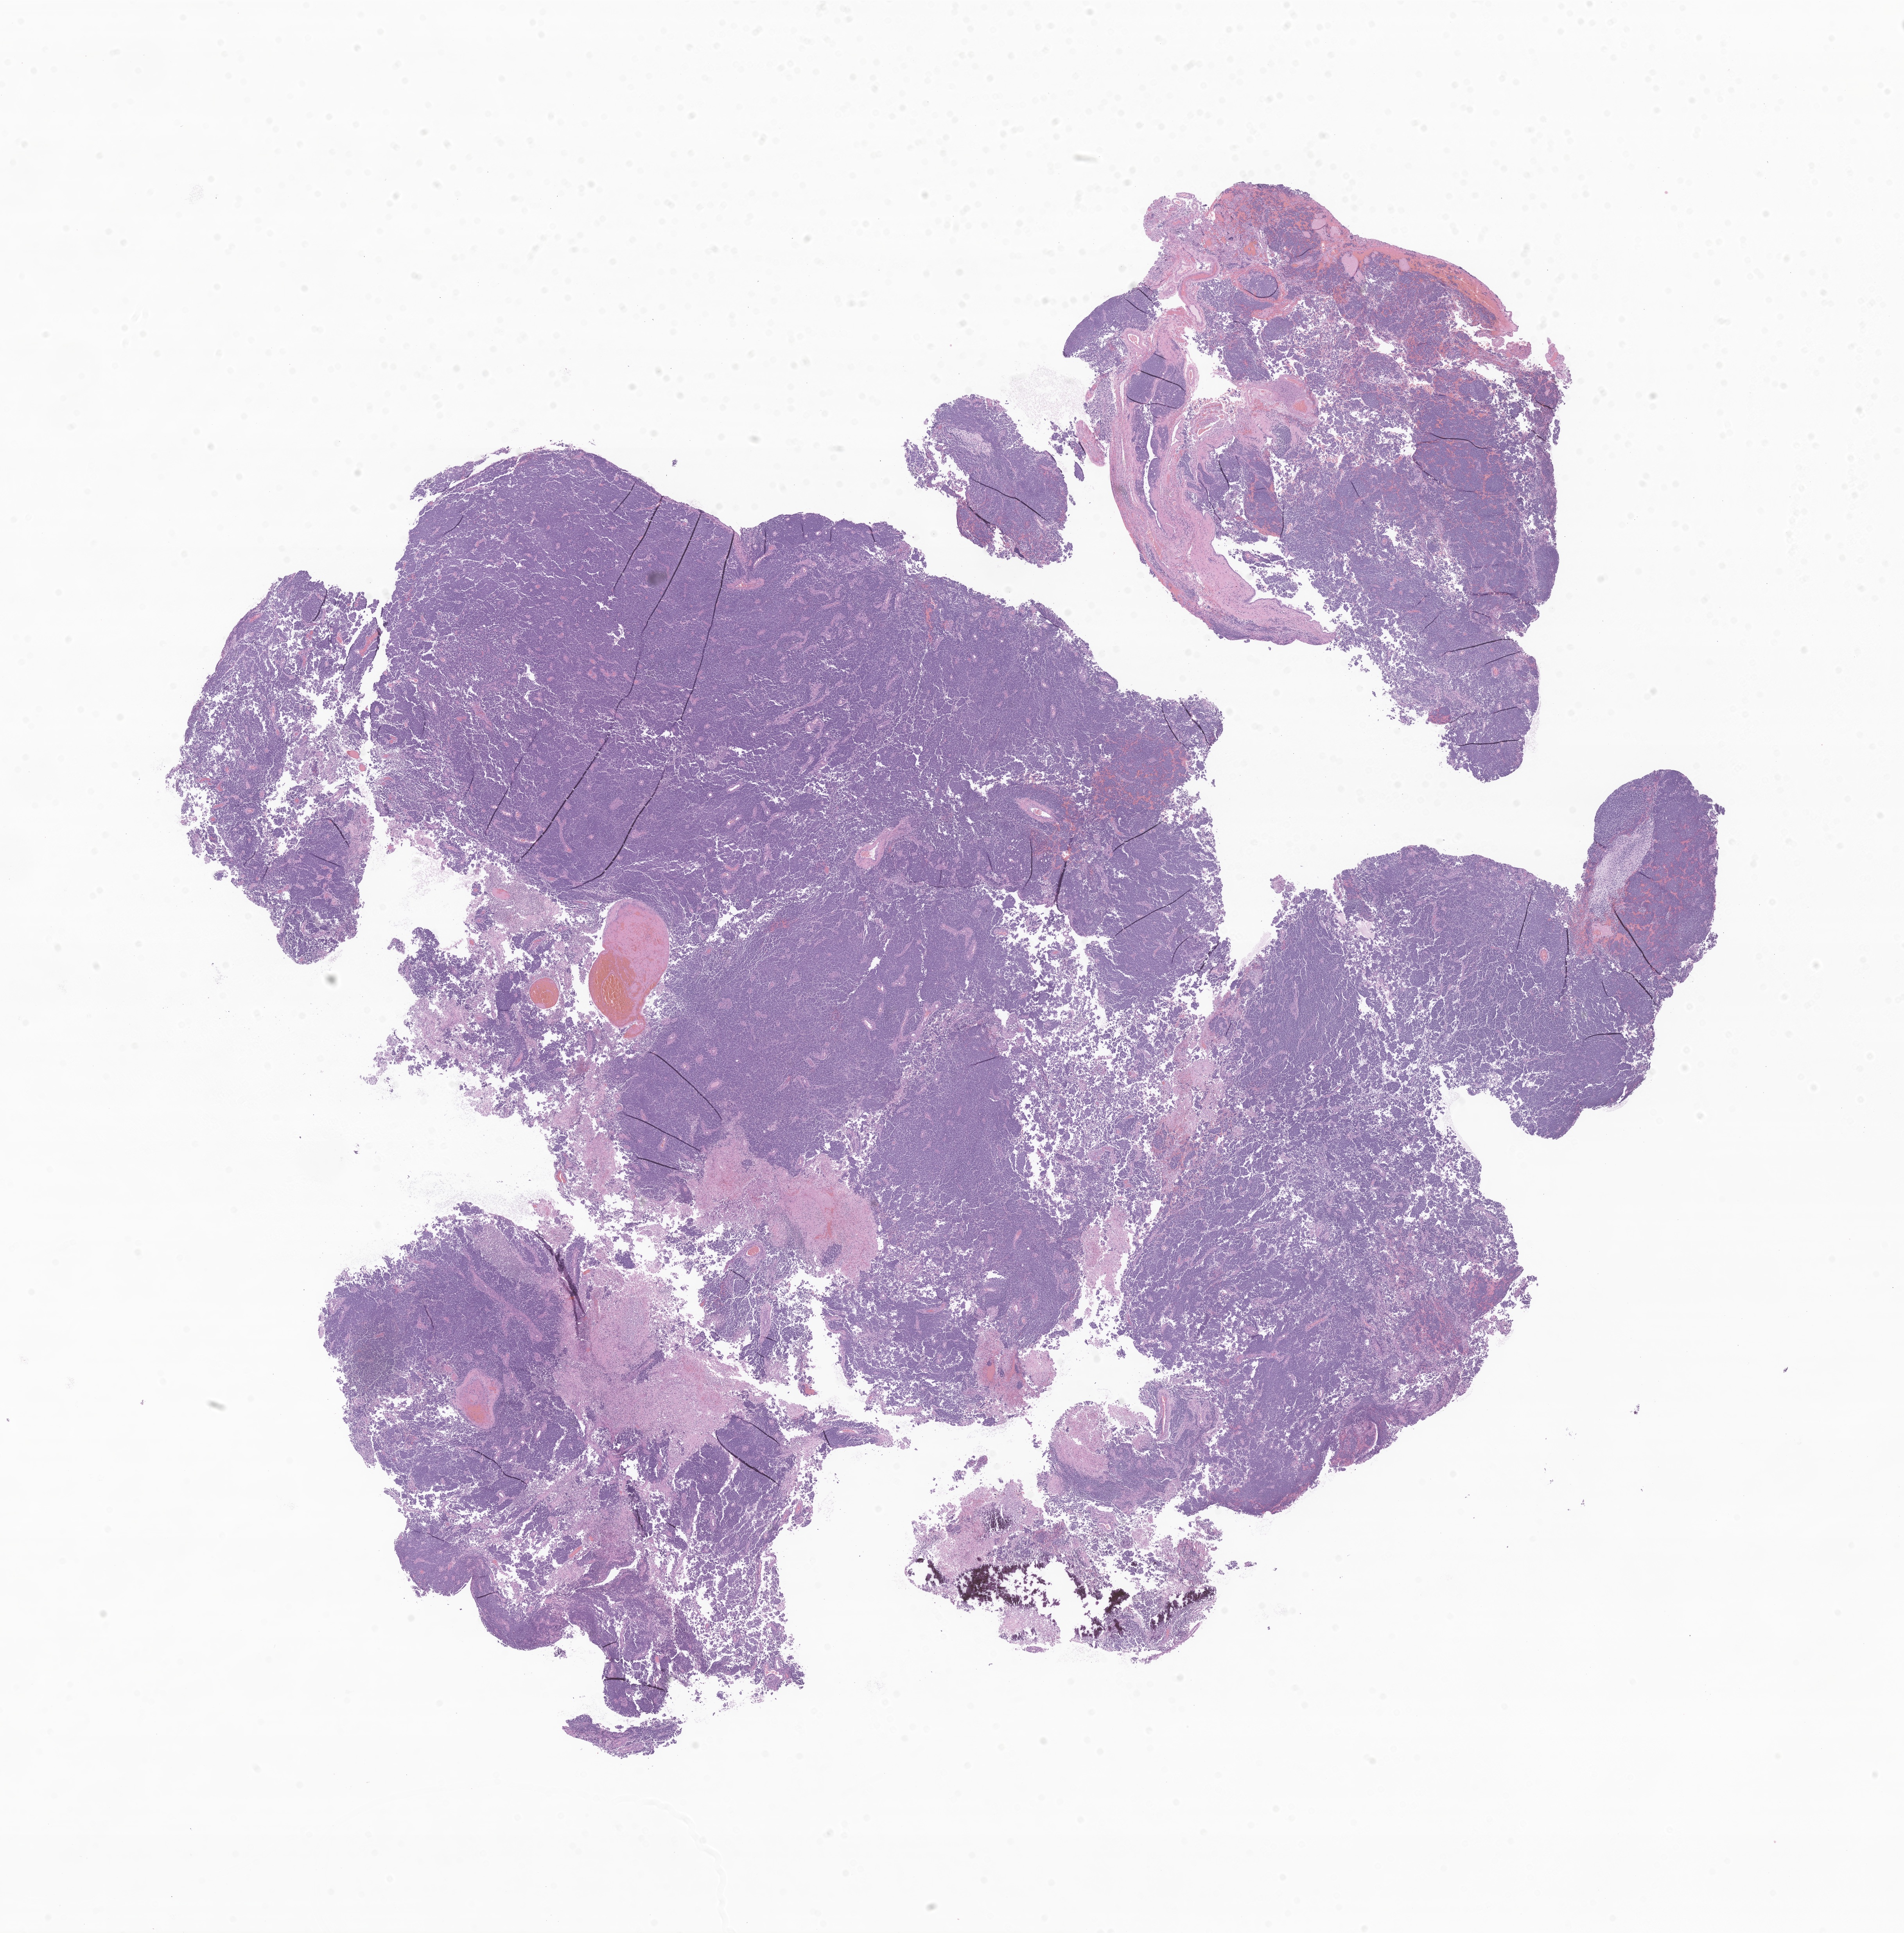
Digitized H&E-stained section of tumor tissue from the brain — low-resolution overview of the scanned area, about 20.5 x 20.8 mm. Formalin-fixed paraffin-embedded section. Patient female; age 817 days (about 2.2 years).
* diagnosis: Neoplasm, malignant